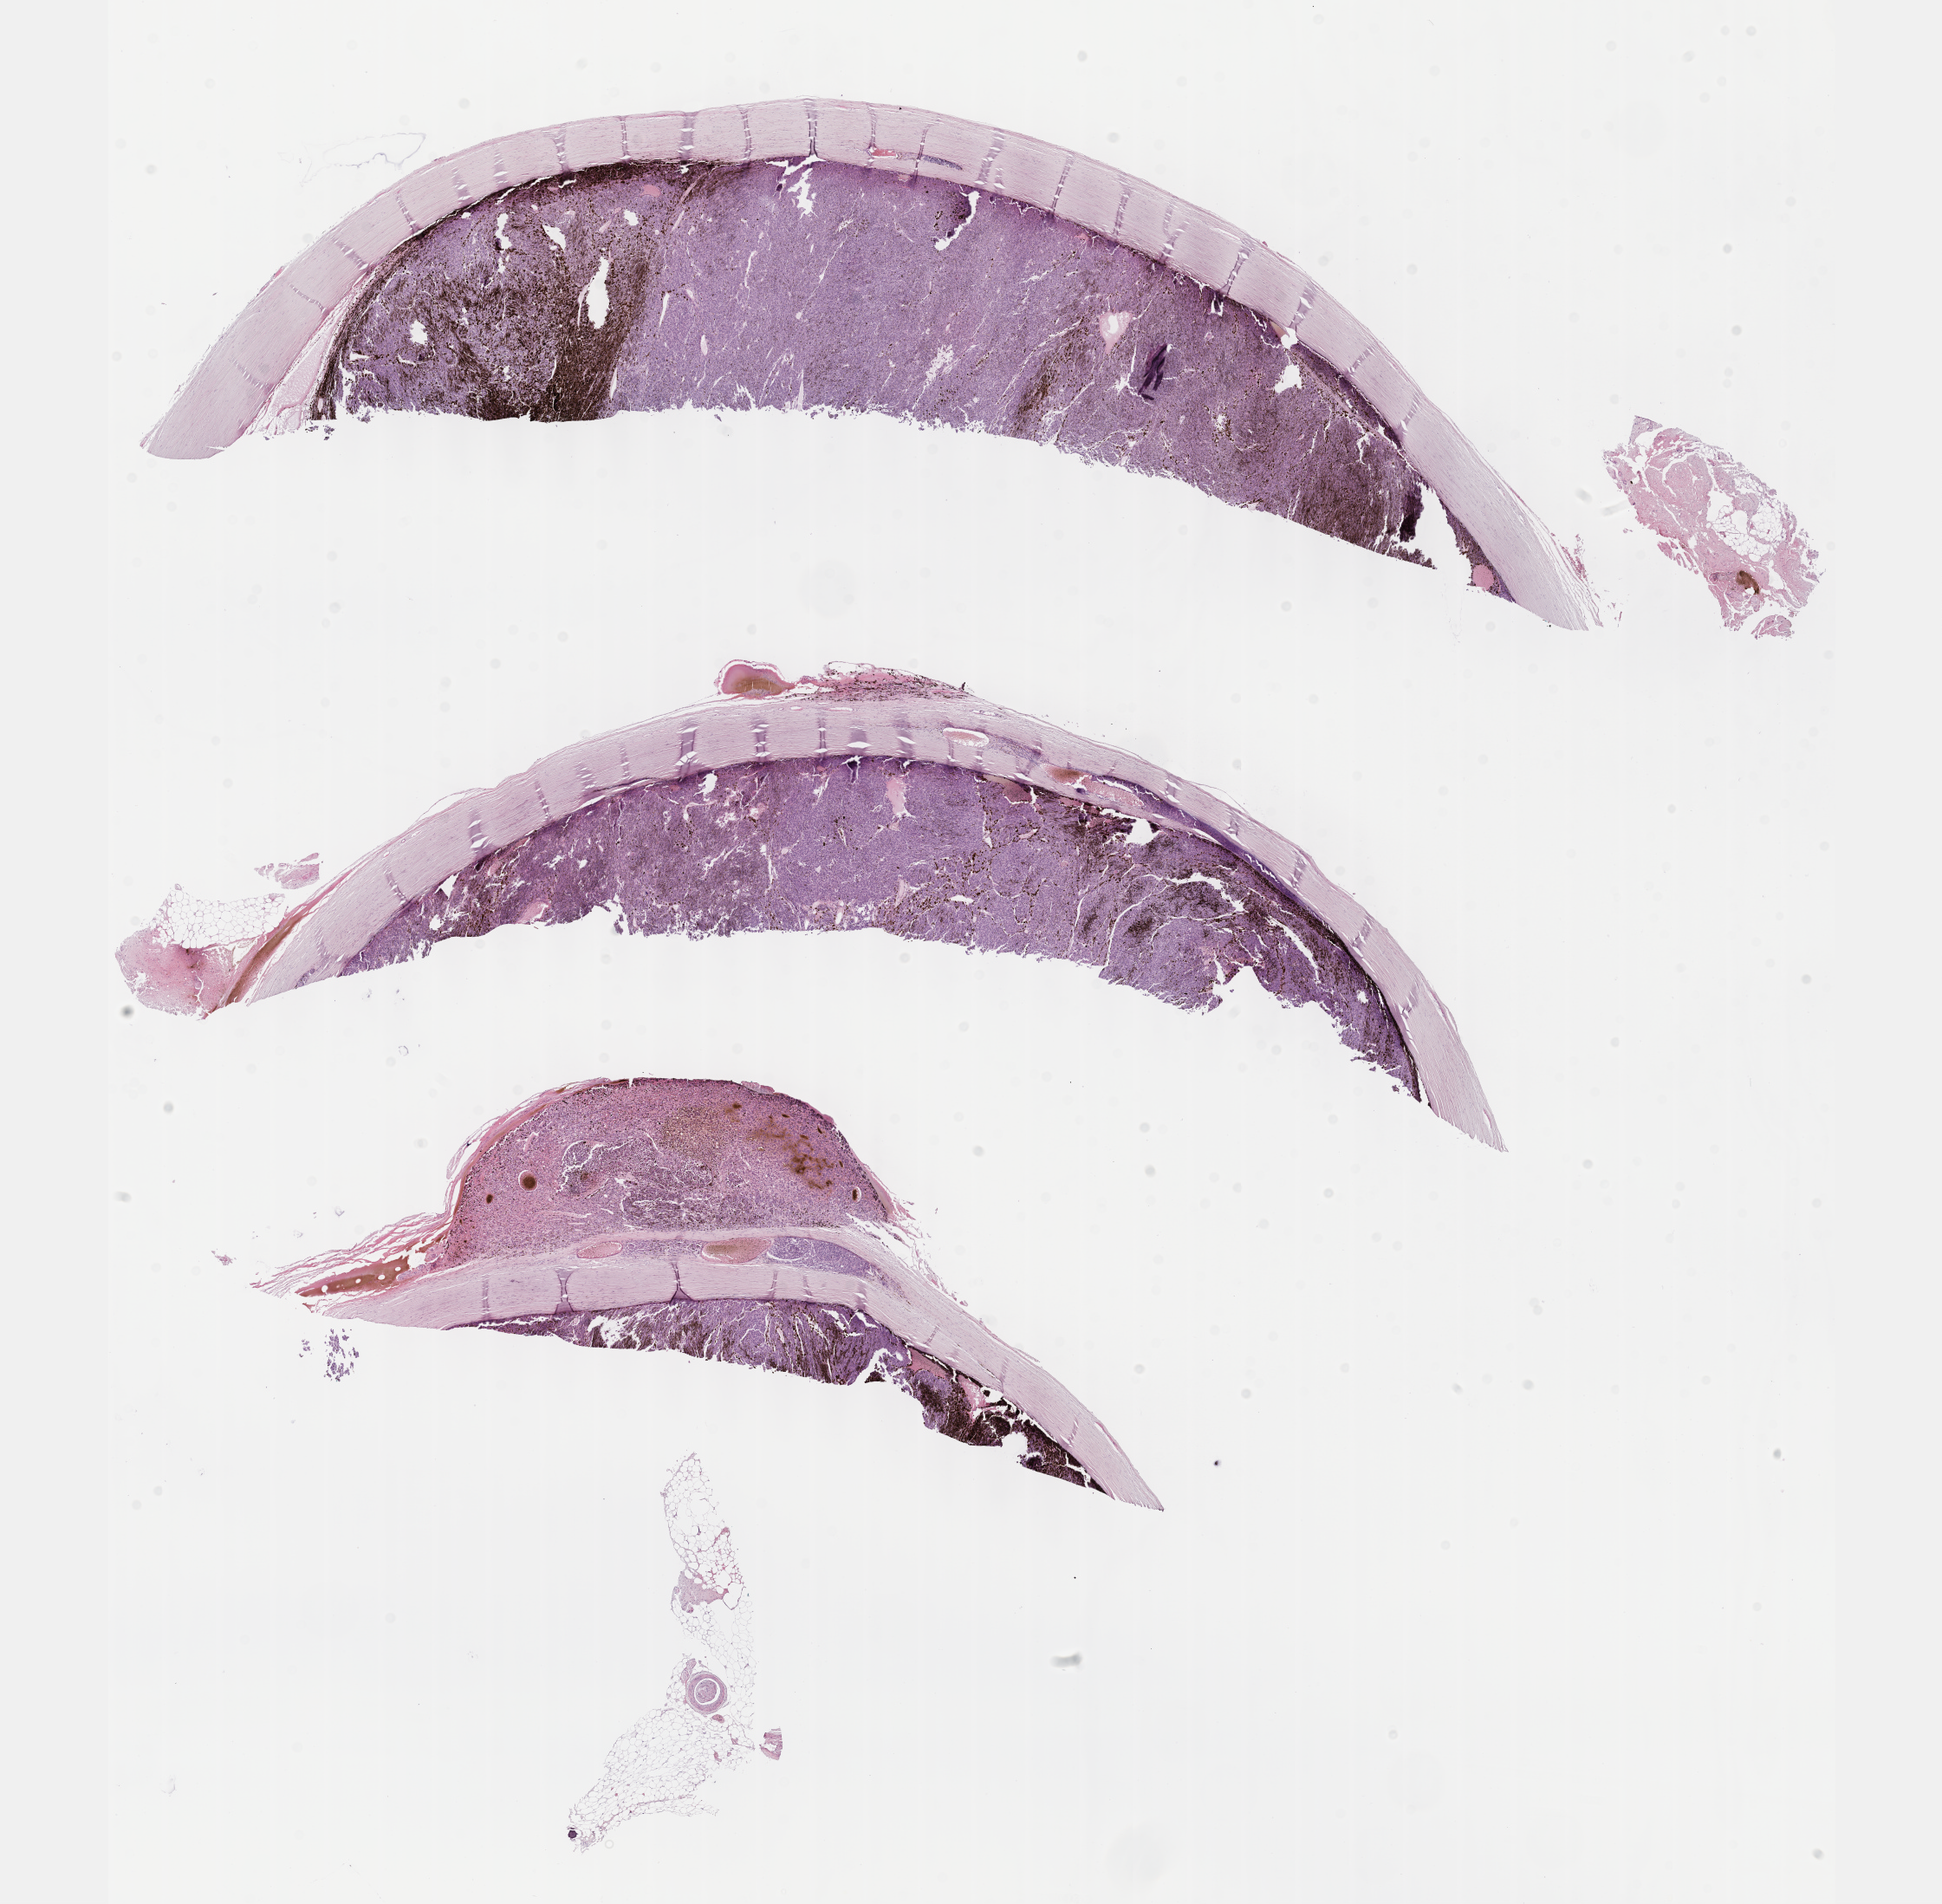
Digitized H&E tissue section (whole slide), whole scanned area (about 18.1 x 17.8 mm) shown as a low-resolution overview. Formalin-fixed paraffin-embedded (FFPE) diagnostic section. Uvea, primary tumour sample. Patient: male, age at initial diagnosis 78 years.
Histologic diagnosis: Epithelioid cell melanoma (choroid). AJCC pathologic stage: IIIB. TNM: T4c N0 M0.